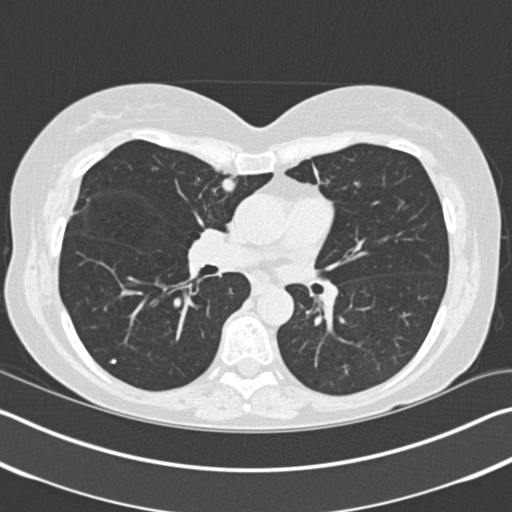
Low-dose screening chest CT, axial slice. Baseline annual screen. Lung window (W 1500 / L -600 HU). Standard (soft-tissue) reconstruction kernel (B30f). 120 kVp. Female participant, aged 61 years at enrolment. Former smoker at enrolment.
- Lesion marked by an expert reader, bounding box <202,169,245,208> (left, top, right, bottom; pixels).
- The screening reader recorded 2 non-calcified nodules or masses ≥4 mm on this exam; which of them this box marks is not recorded.
- Lung cancer was diagnosed 131 days after this screen: adenocarcinoma, NOS, right upper lobe, stage IA (AJCC 6th edition), 11 mm at pathology.